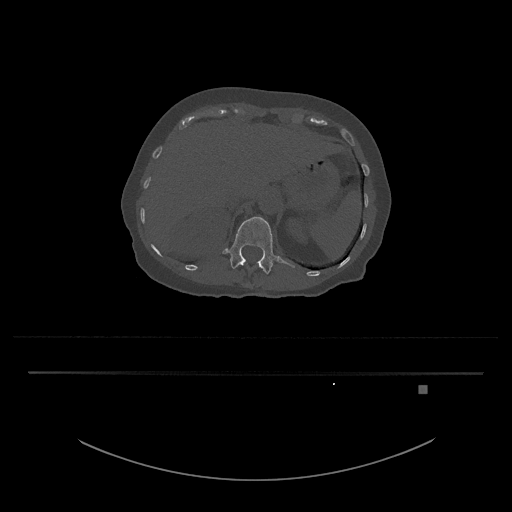
CT including the spine, one axial slice. Slice 566 of 797 in the series (ordered by position). Reconstruction kernel Br40s/3. Bone window (W 1800 / L 400 HU). 512 × 512 image matrix, field of view 500 × 500 mm. Patient: female, 57 years. Case-level facts recorded for this patient, not image findings: primary cancer: cervical.
Outlined on this slice (semi-automatic segmentation, software-assisted and operator-edited):
- L1 vertebra: bounding box <222,217,295,274> (left, top, right, bottom; pixels)
- T12 vertebra: <243,263,263,269>